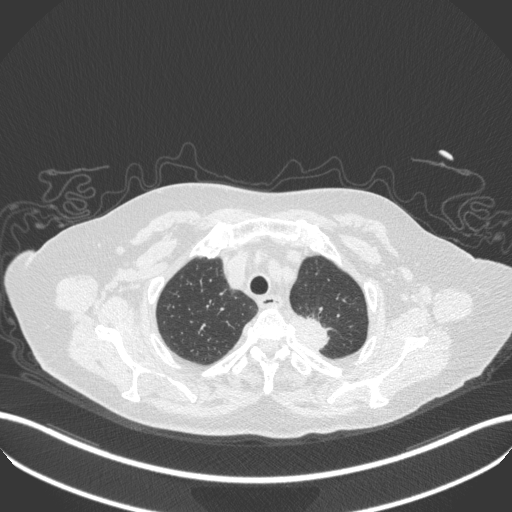
Chest CT, one axial slice. Slice 290 of 353 in the series (ordered by position). 100 kVp. Lung window (W 1500 / L -600 HU). 512 × 512 image matrix, field of view 400 × 400 mm. Patient: female, 81 years. From the clinical record (not read from this slice): clinical TNM (as recorded): T2a N0 M0.
Outlined on this slice (rectangle marked by the reading radiologist):
- lung tumour (recorded histology: adenocarcinoma): box from (x=283, y=307) to (x=336, y=350) px